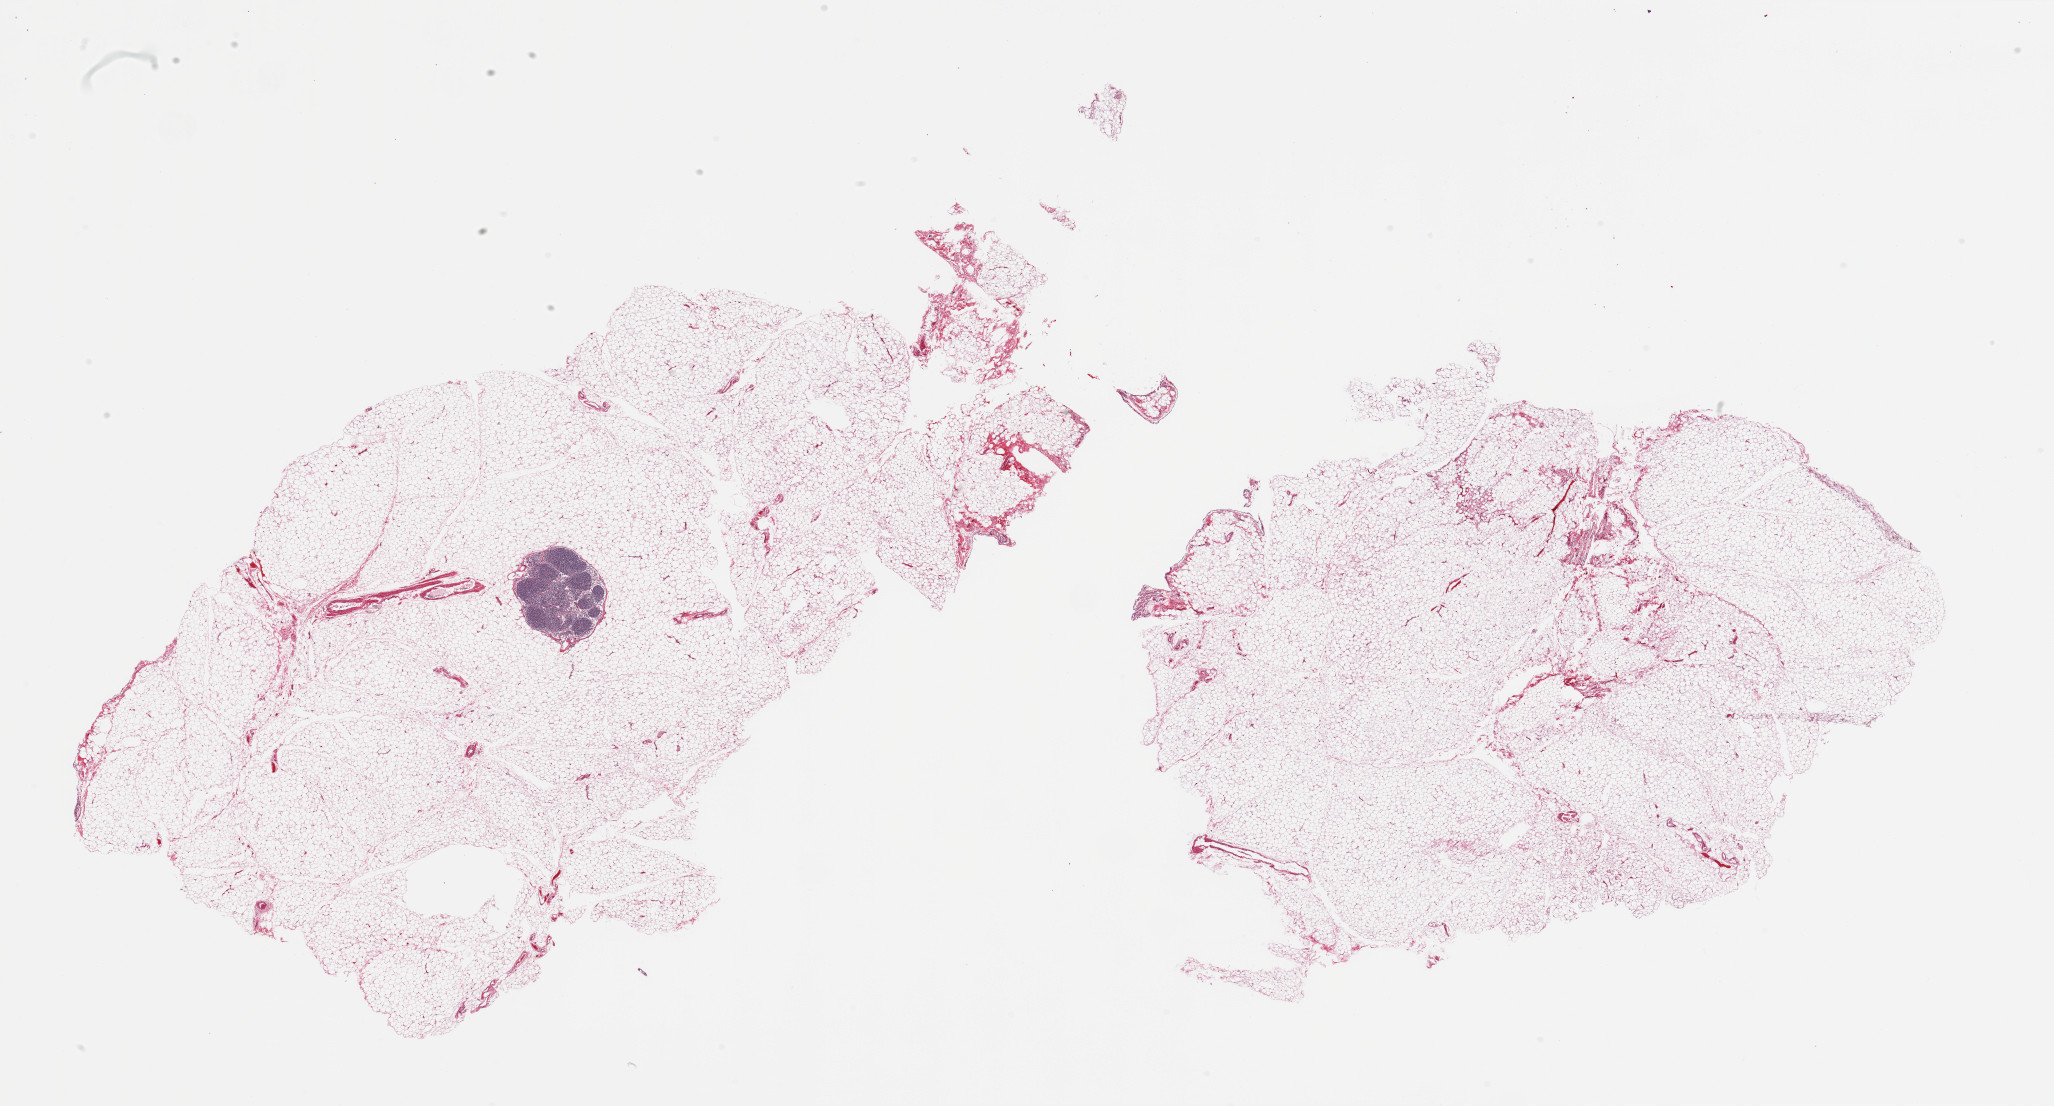
Digitized hematoxylin and eosin (H&E)-stained section — shown as a low-resolution overview of the whole scanned area (about 32.5 x 17.5 mm, acquisition: 20x scan); PAXgene-fixed paraffin-embedded (PFPE) section; target tissue: omentum; donor tissue sample. Male donor.
* review note (as recorded): 2 pieces; mature adipose tissue and small 1.6mm in diameter lymph node; ~5% fibrovascular component